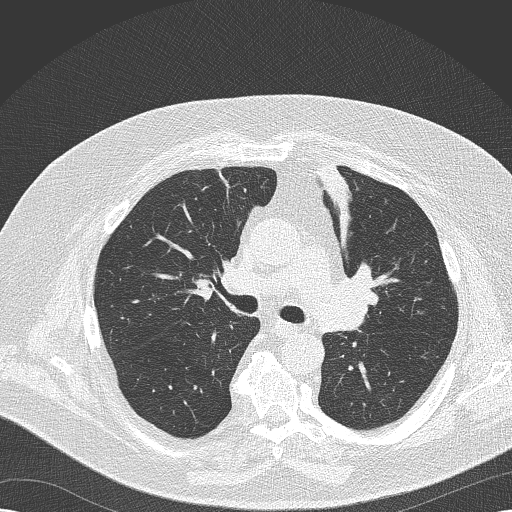
Low-dose screening chest CT, axial slice, second annual screen, lung window (W 1500 / L -600 HU), 2 mm slice thickness, lung (sharp) reconstruction kernel (B50f), 120 kVp. Male participant, aged 68 years at enrolment.
Lesion marked by an expert reader, bounding box (x1, y1, x2, y2) in pixels: (321, 265, 381, 327). Screening reader's record for this exam (one nodule recorded; not confirmed to be the boxed lesion): non-calcified nodule or mass ≥4 mm, left lower lobe, 8 × 6 mm, soft tissue attenuation, pre-existing on the prior screen: yes; interval growth: no. Participant outcome: lung cancer diagnosed 256 days after this screen — squamous cell carcinoma, NOS, left upper lobe, poorly differentiated (G3), stage IIB (AJCC 6th edition), 35 mm at pathology.